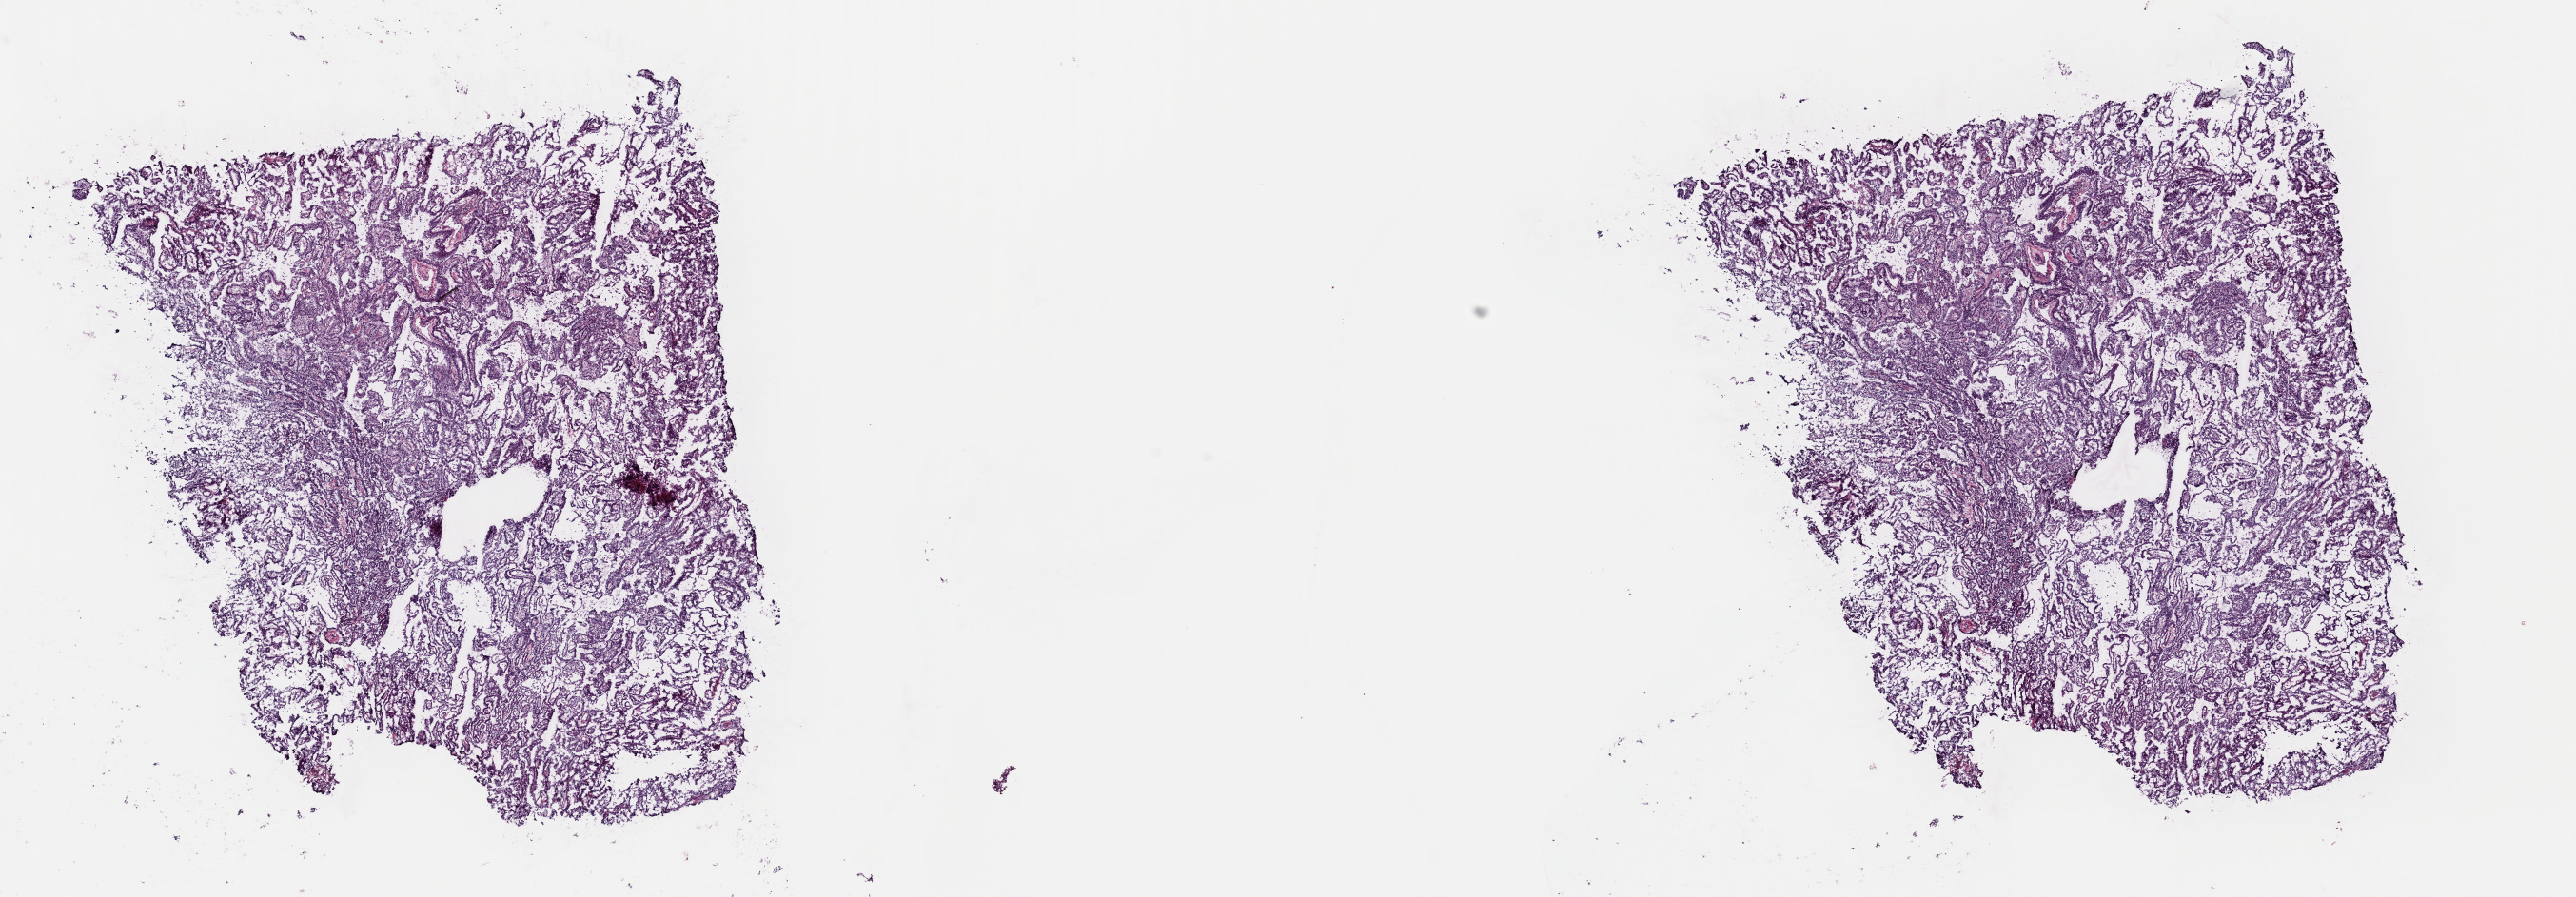
H&E whole-slide image, shown as a low-resolution overview of the whole scanned area (about 21.4 x 7.4 mm, slide scanned at 40x). Frozen section from the top of the tissue portion. Sample: primary tumour, kidney. Male patient; age at initial diagnosis 56 years. Composition of this section per pathologist review: tumour cells 90%, tumour nuclei 90%, normal cells 0%, stromal cells 10%, necrosis 0%. Inflammatory infiltration, as recorded: lymphocyte infiltration 0%, monocyte infiltration 0%, neutrophil infiltration 0%.
- lymph nodes positive (case pathology): 0 of 7 examined
- AJCC pathologic stage: III (7th edition)
- diagnosis: Papillary adenocarcinoma, NOS